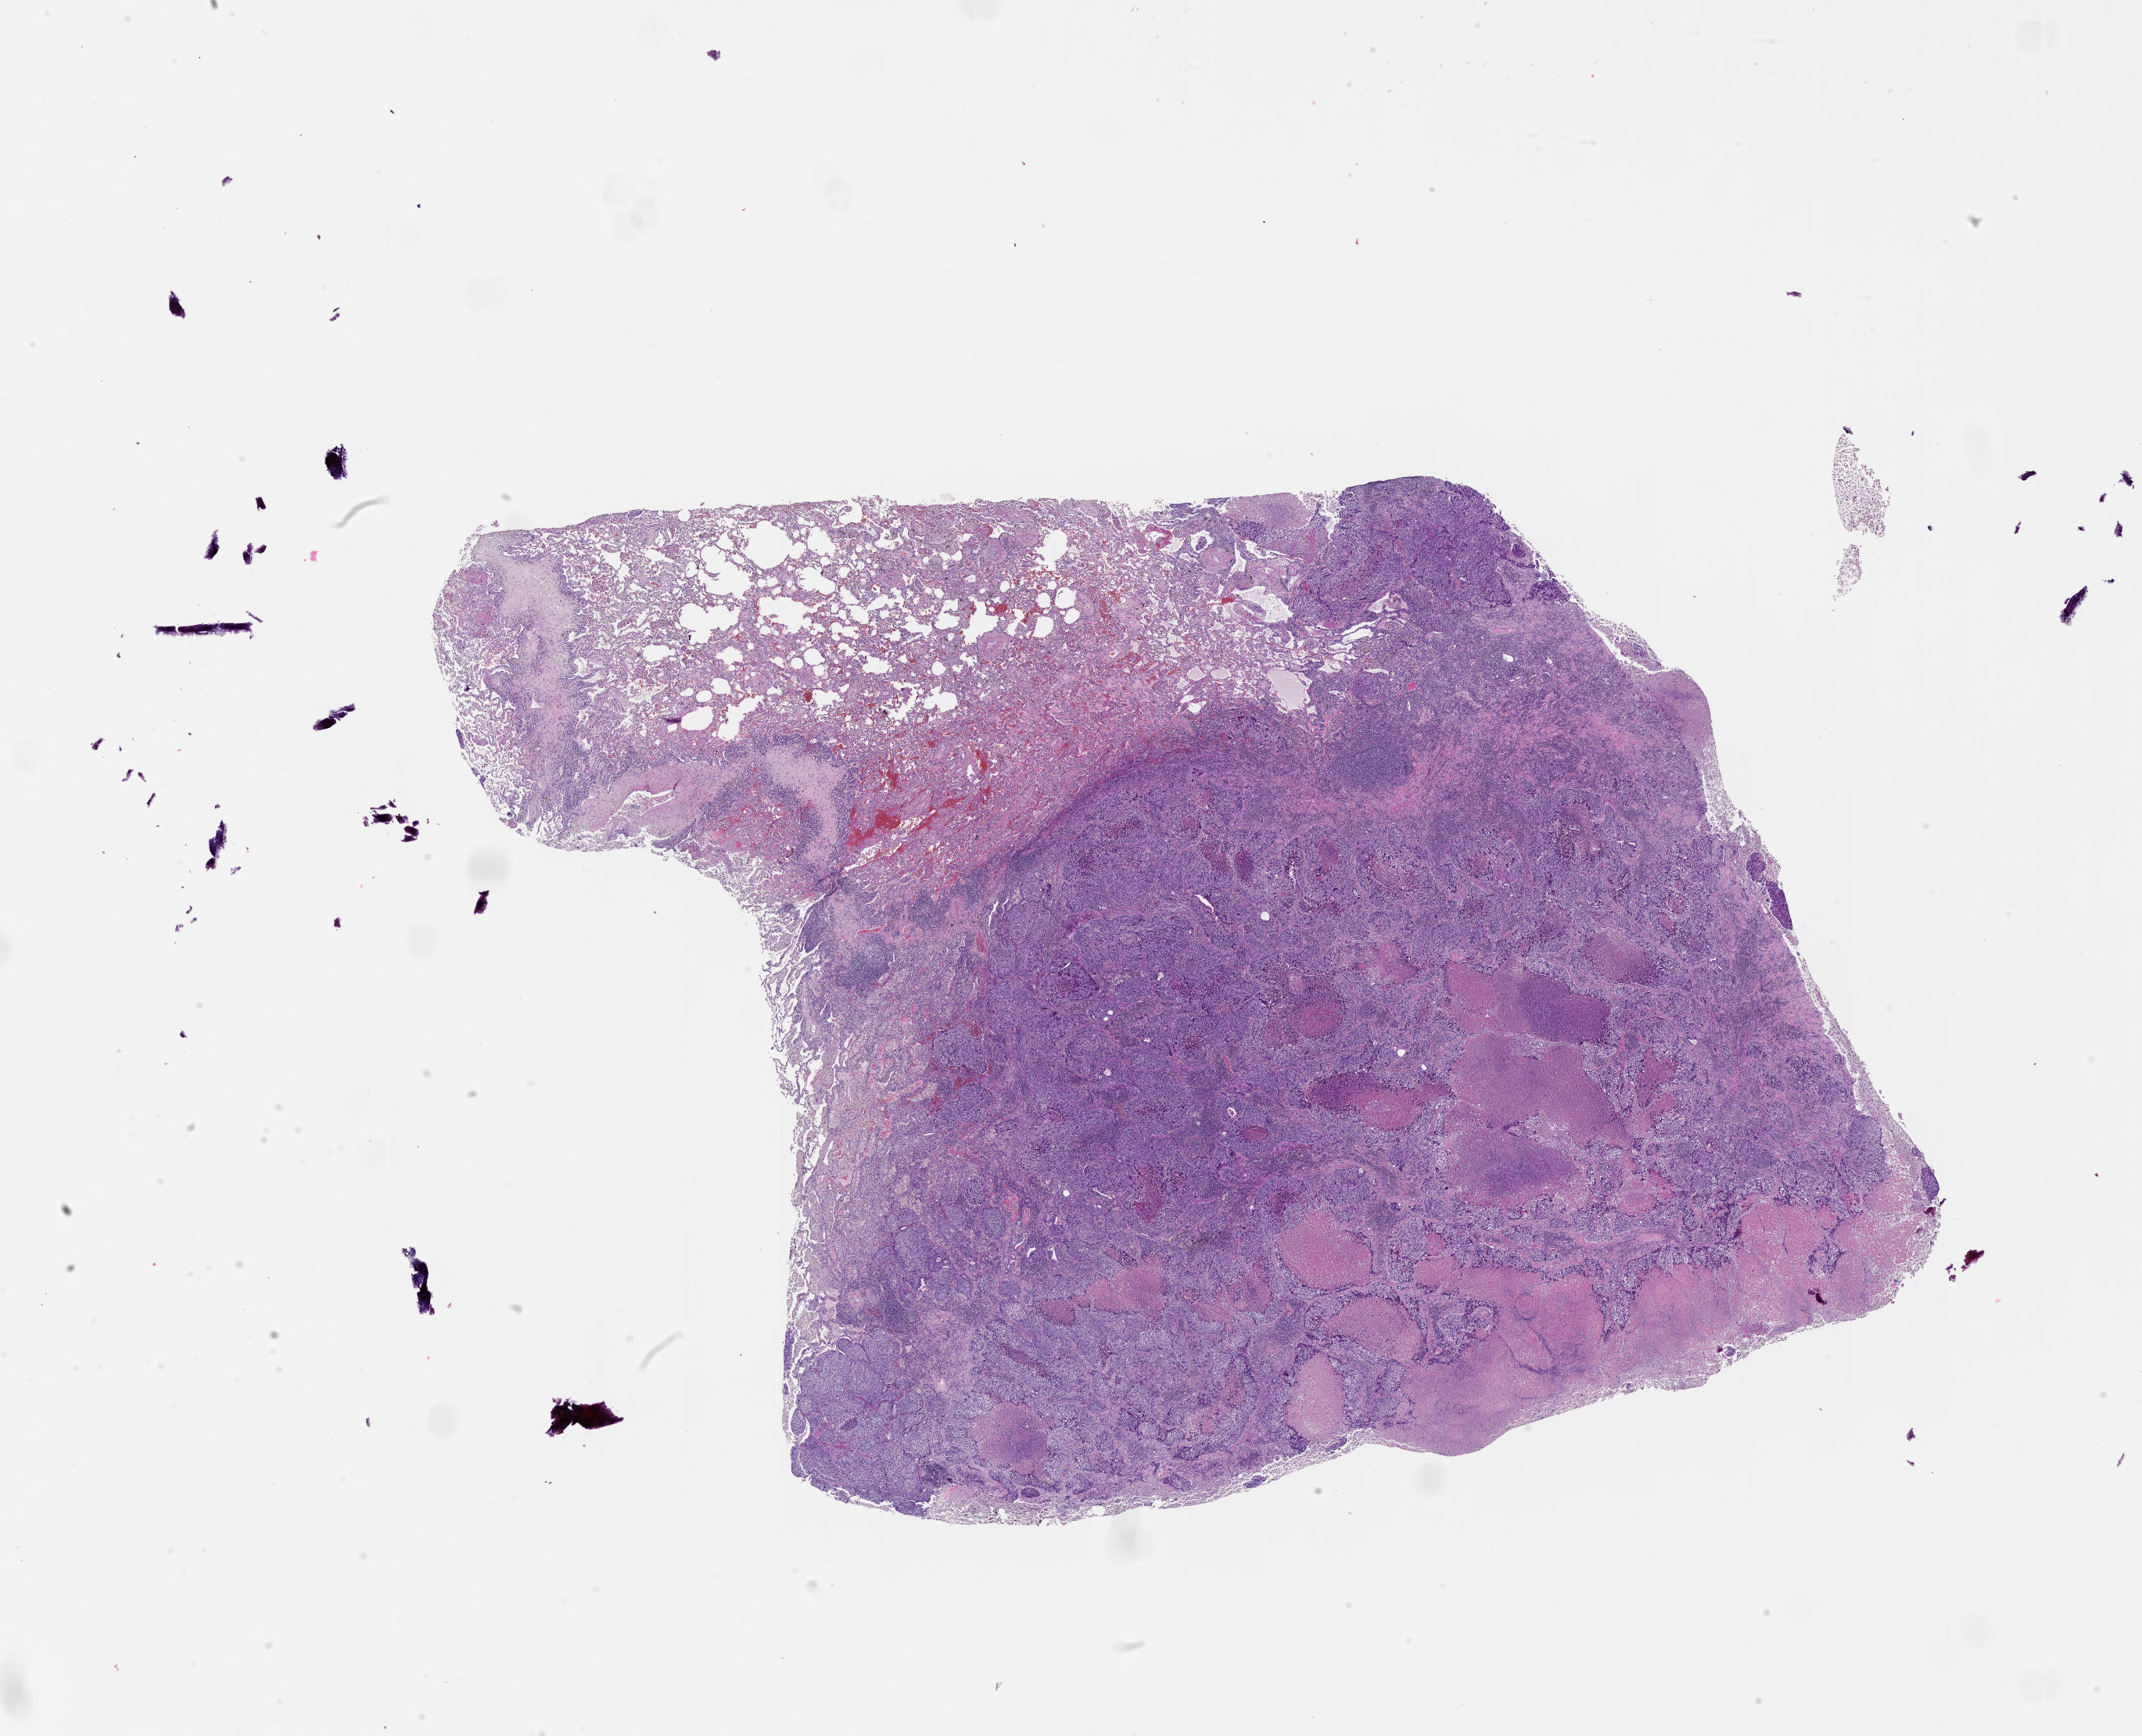
Digitized Hematoxylin and eosin (H&E) stained tissue section (whole slide), whole scanned area (about 22.0 x 17.9 mm, slide scanned at 20x) shown as a low-resolution overview; tumour tissue sample, lung. Patient: male, age 54 years.
Patient diagnosis (cohort enrolment): squamous cell carcinoma (lung).